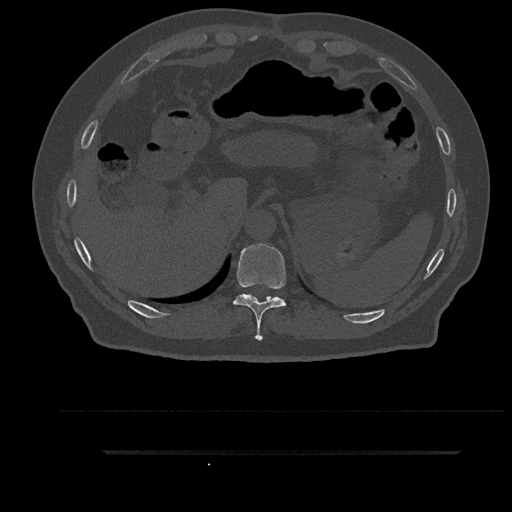
CT including the spine, one axial slice. Position 357 of 797 along the scan axis. 120 kVp. Bone window (W 1800 / L 400 HU). 512 × 512 image matrix, field of view 432 × 432 mm. Patient: male, 63 years. Case-level facts recorded for this patient, not image findings: primary cancer: renal.
Outlined on this slice (semi-automatic segmentation, software-assisted and operator-edited):
- T10 vertebra: bounding box (x1, y1, x2, y2) in pixels: (233, 244, 286, 340)
- T11 vertebra: (246, 294, 255, 298)